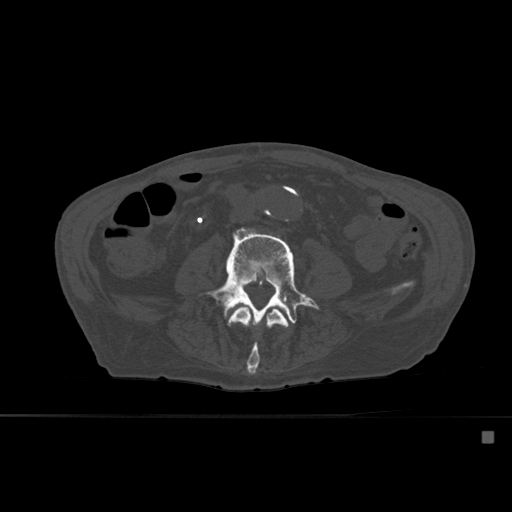
CT including the spine, one axial slice; position 198 of 527 along the scan axis; bone window (W 1800 / L 400 HU); 512 × 512 image matrix, field of view 373 × 373 mm. Patient: male, 78 years. Case-level facts recorded for this patient, not image findings: primary cancer: prostate.
Annotated regions visible in this slice (semi-automatically segmented with operator editing):
- L3 vertebra: box from (x=228, y=306) to (x=289, y=375) px
- L4 vertebra: (x=200, y=227)–(x=320, y=324)